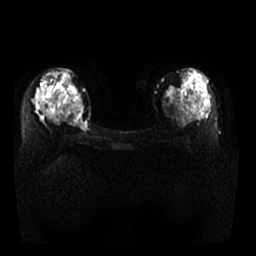
Breast MRI, one axial slice; slice 17 of 29 in the series (ordered by position); diffusion-weighted series; image 2 of 4 stored at this slice position (different b-values; order by instance number); 1.5 T; 4 mm slice thickness; 256 × 256 image matrix, field of view 340 × 340 mm. Female patient.
Annotated regions visible in this slice (outlined manually by an expert reader):
- tumour on diffusion-weighted imaging: bounding box [x1, y1, x2, y2] px = [67, 88, 87, 131]